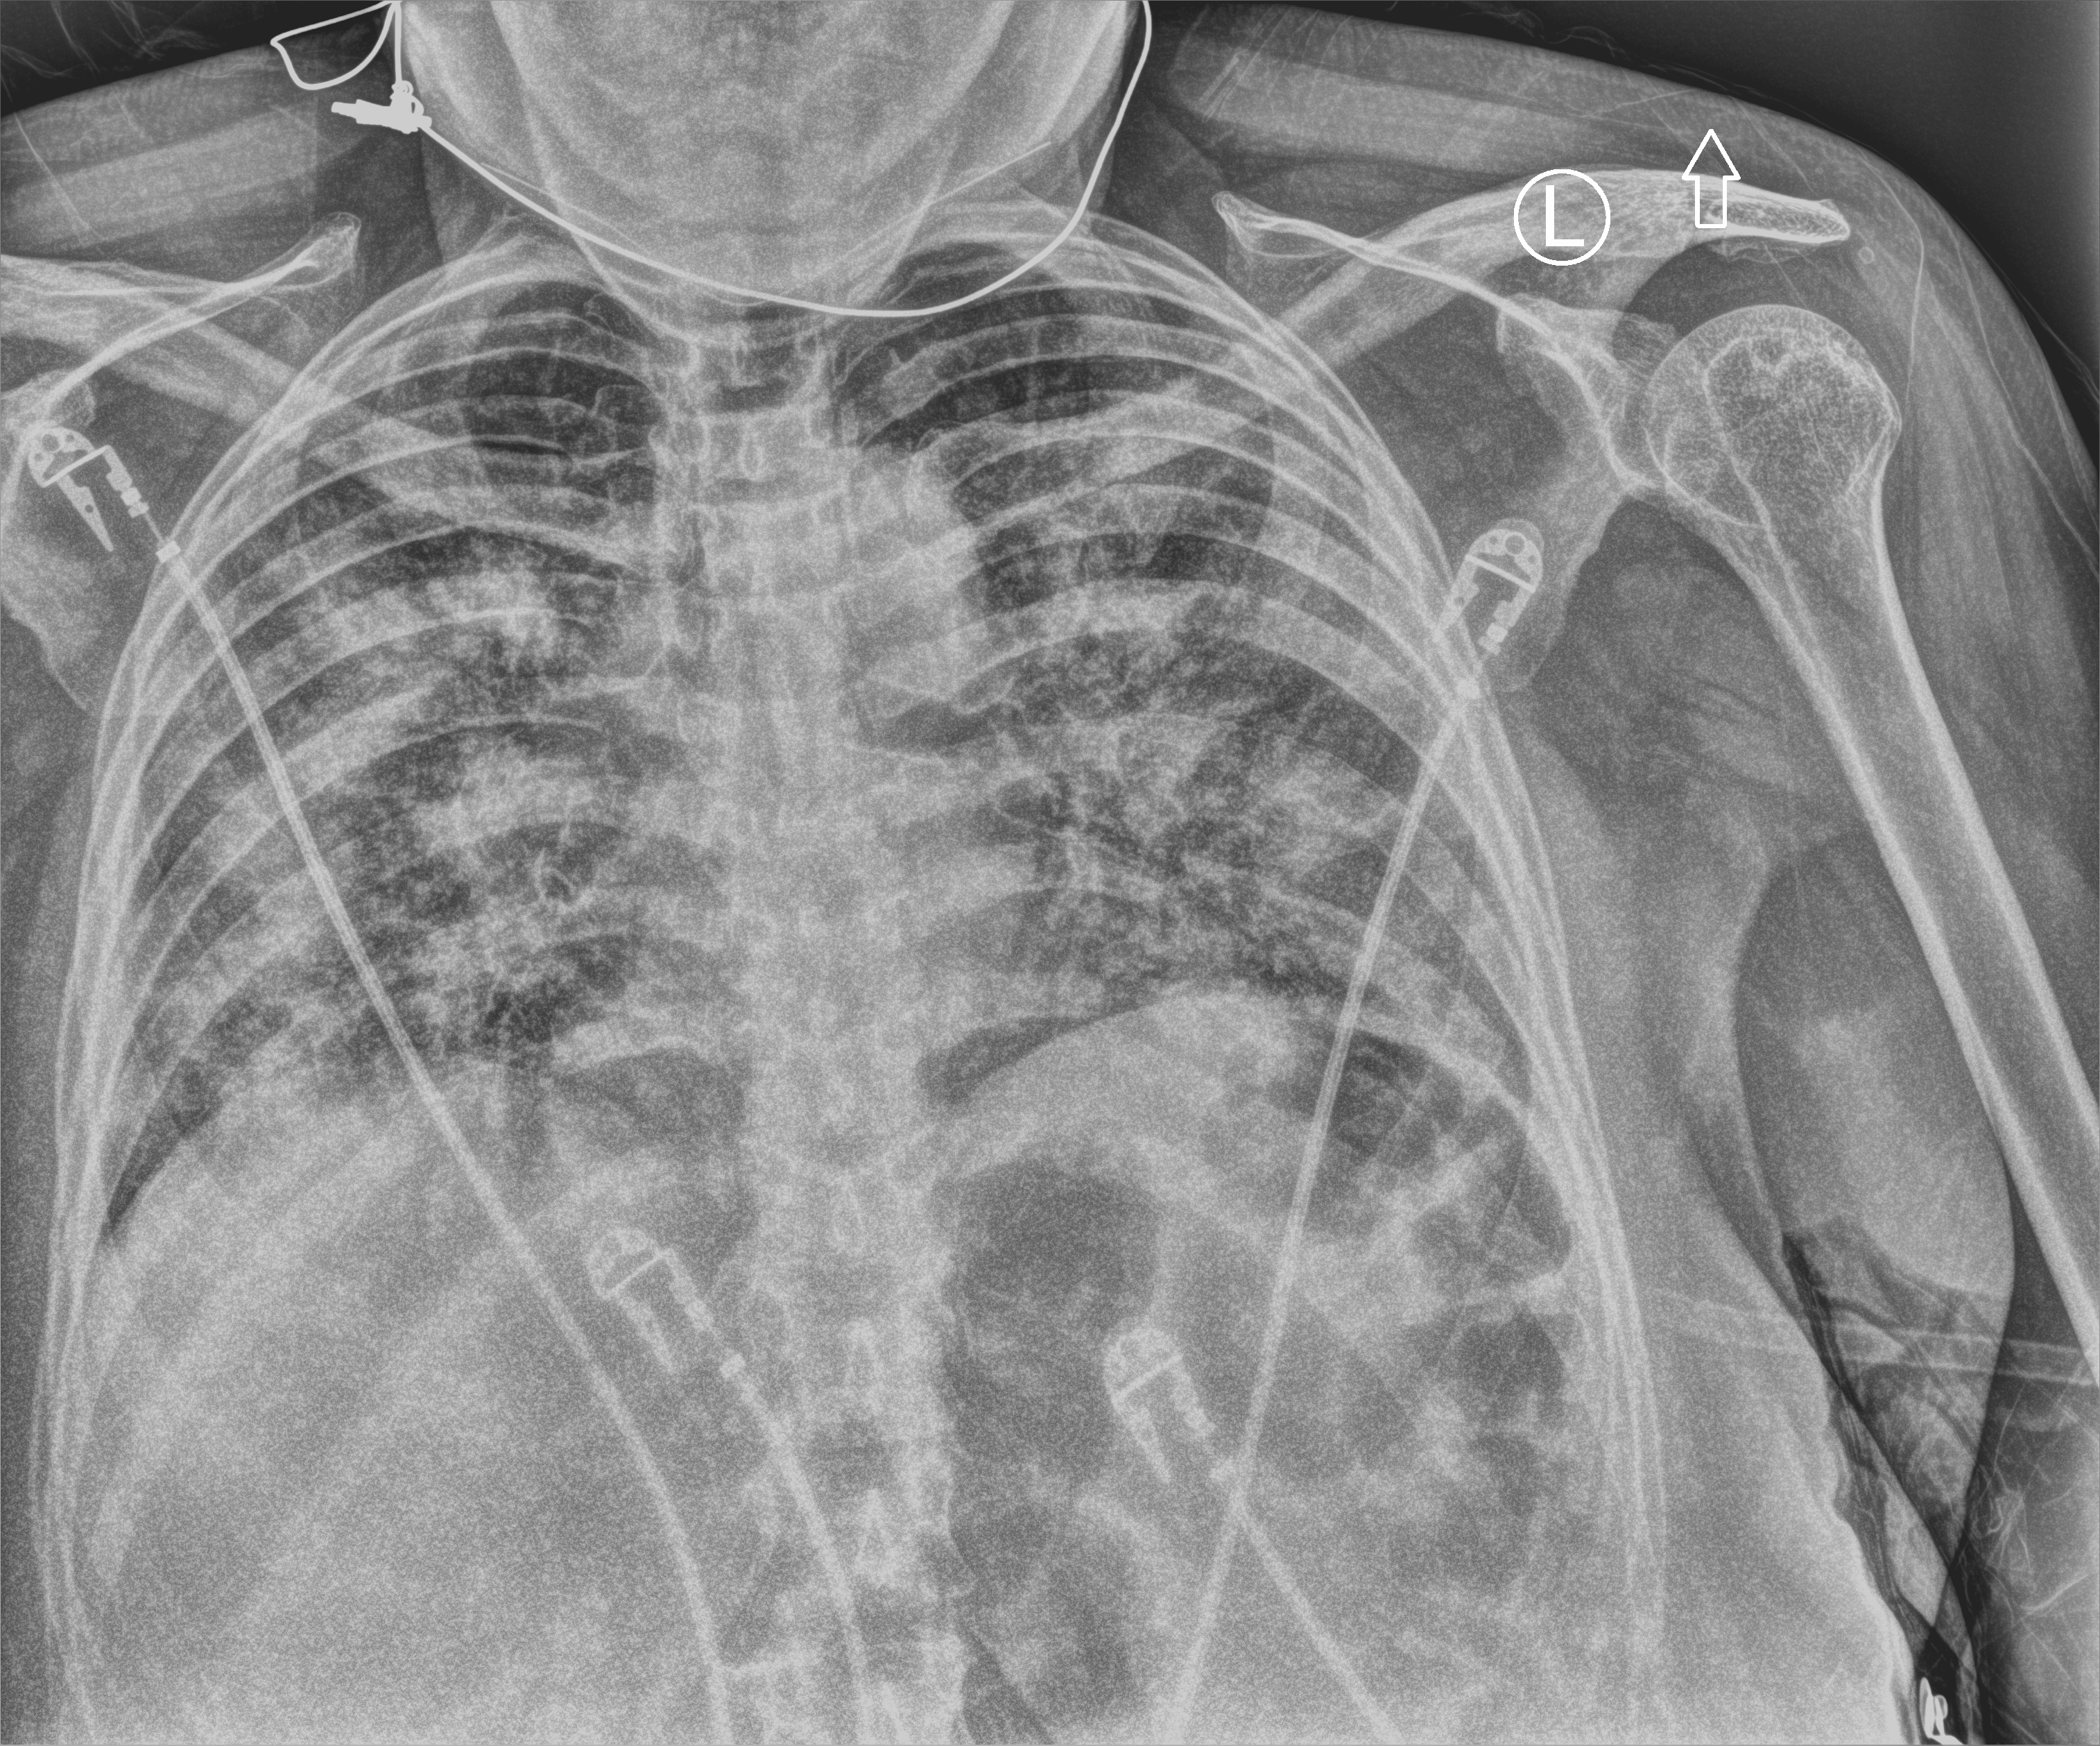
Bedside chest radiograph (computed radiography), anteroposterior (AP) projection. Patient hospitalised with COVID-19; female, aged 75–90 years.
Hospital-stay facts (about this admission, not read from this image; timing relative to this image not recorded): admitted to intensive care during this hospital stay: yes; other chronic lung disease (admission record): no; mechanically ventilated during this hospital stay: yes.